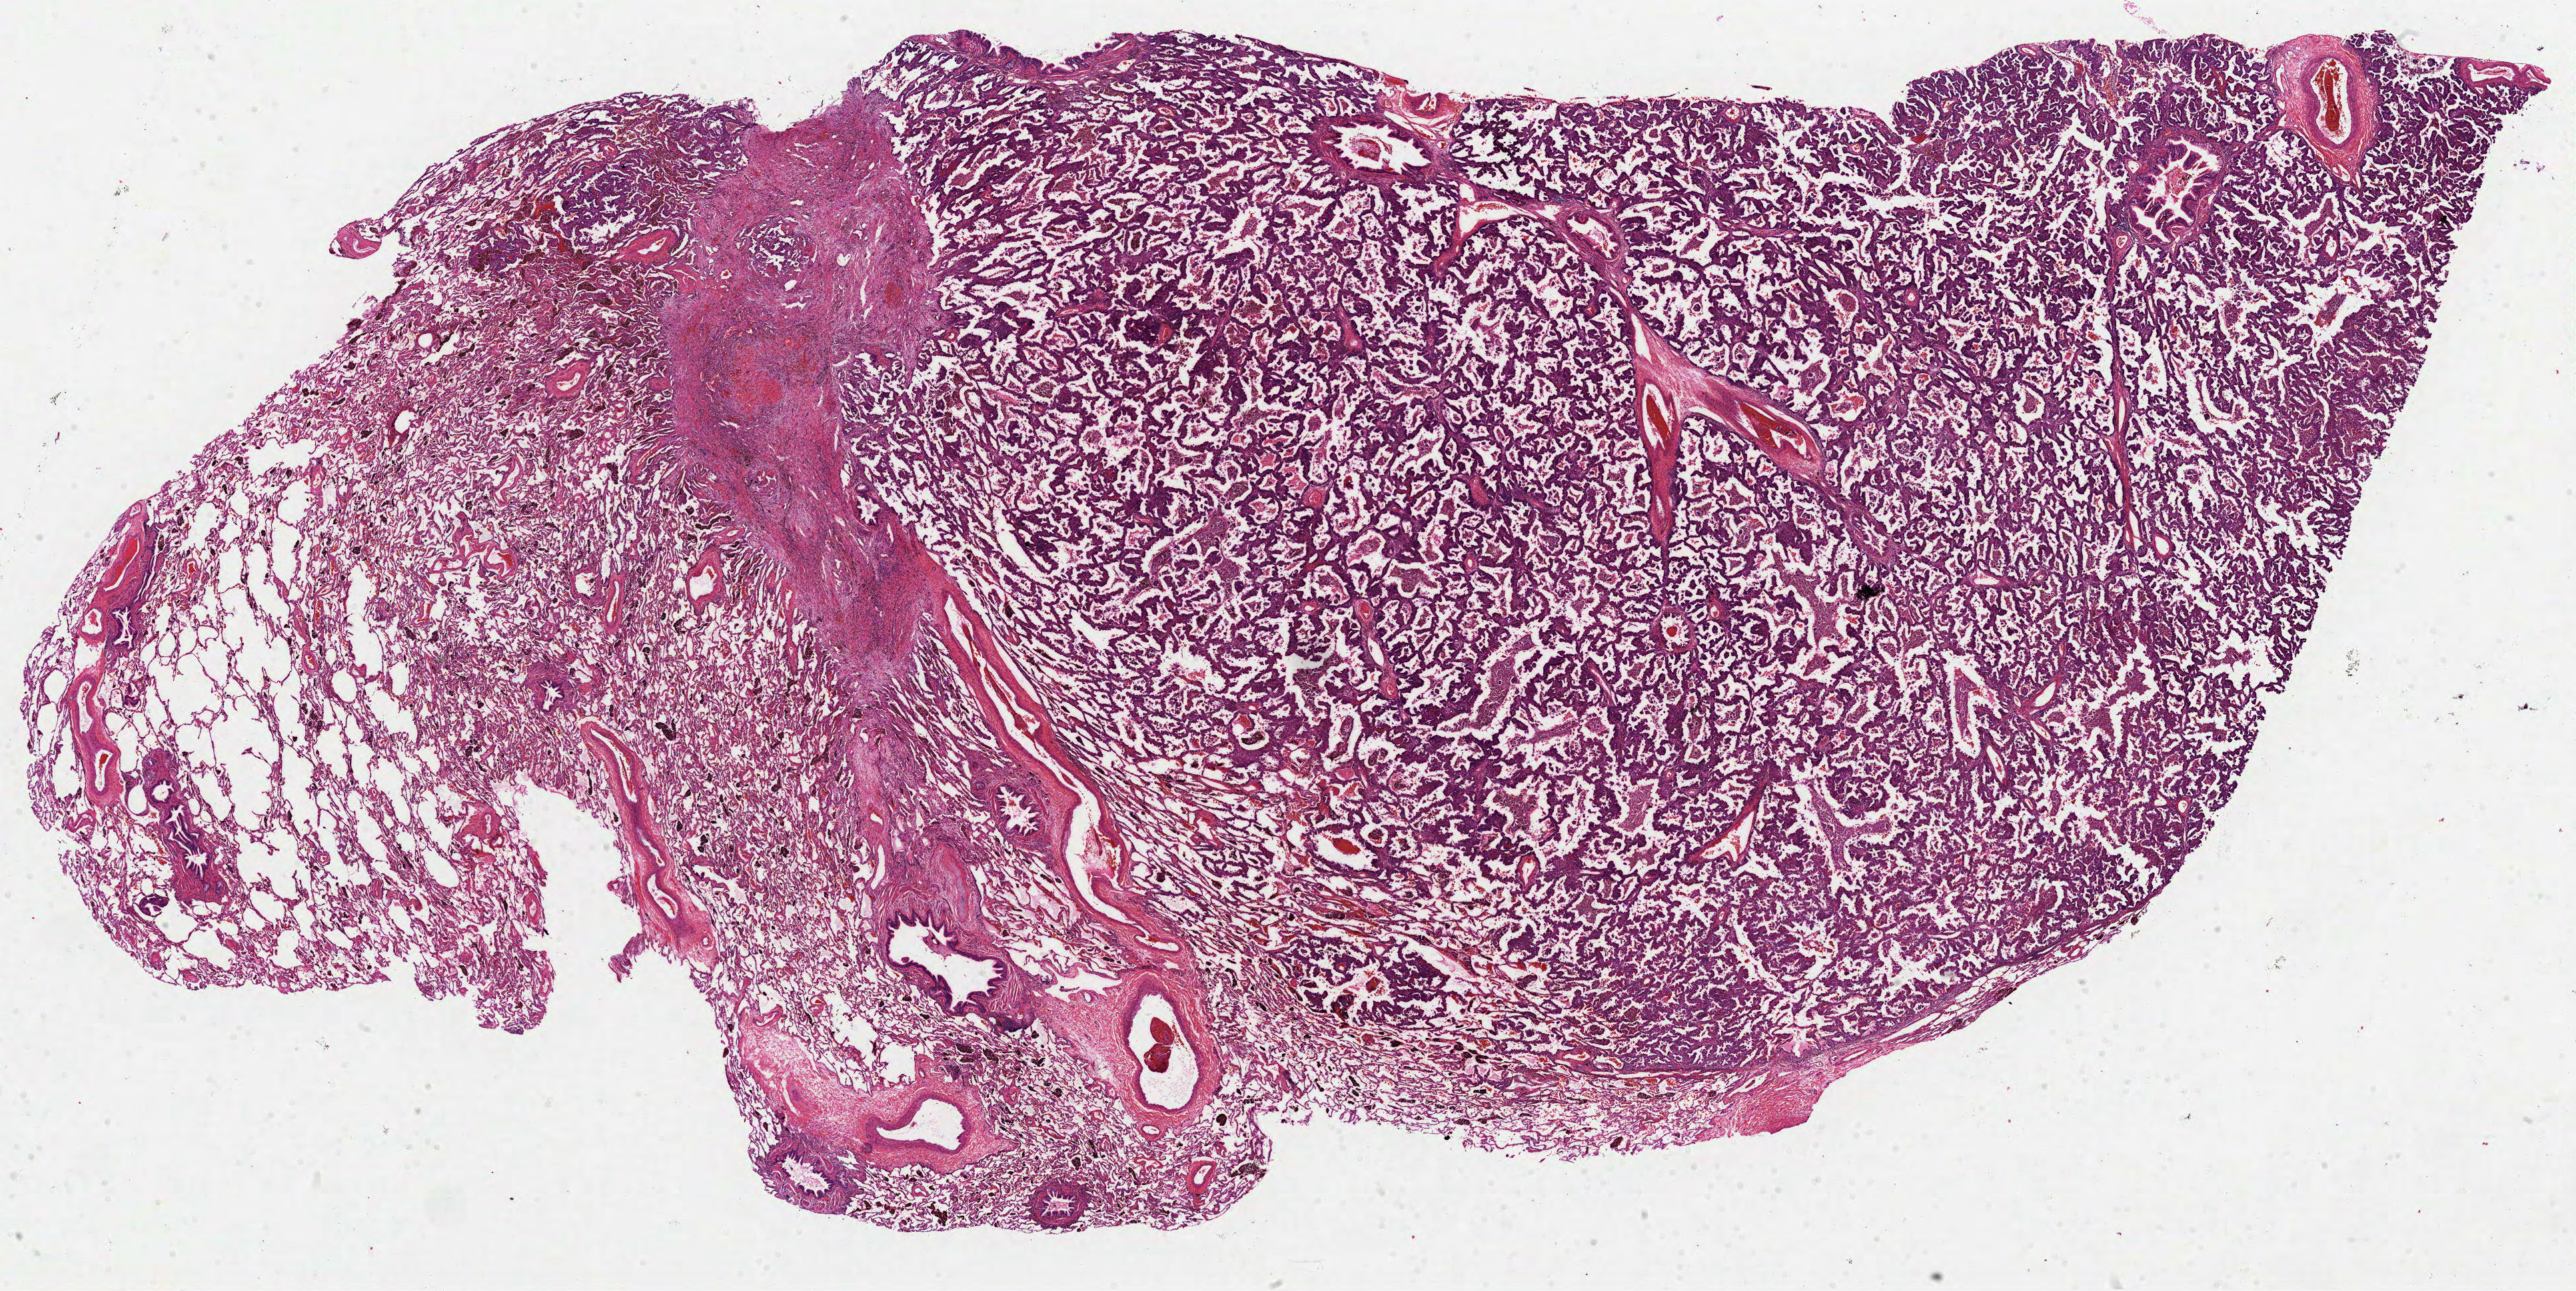
Hematoxylin and eosin (H&E) stained whole-slide image — a low-resolution overview of the entire scanned area, about 31.2 x 15.6 mm (acquisition: 40x scan); formalin-fixed paraffin-embedded (FFPE) diagnostic section; primary tumour sample from the lung. Female, age 51 years at initial diagnosis.
AJCC pathologic stage: IIB (5th edition). Diagnosis: Adenocarcinoma, NOS (upper lobe, lung). Laterality: left.